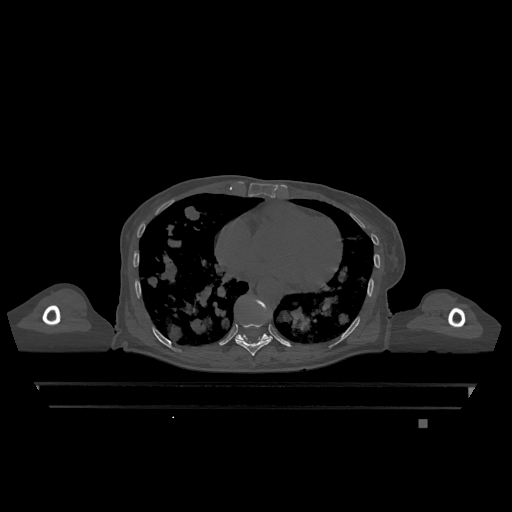
CT including the spine, one axial slice; slice 676 of 1317 in the series (ordered by position); bone window (W 1800 / L 400 HU); 512 × 512 image matrix, field of view 500 × 500 mm. Patient: female, 74 years. From the clinical record (not read from this slice): primary cancer: lung; vertebrae with lytic lesions (as recorded): T1, T4, T5, T6, L4, L5.
Annotated regions visible in this slice (semi-automatic segmentation, software-assisted and operator-edited):
- T10 vertebra: bounding box [x1, y1, x2, y2] px = [235, 299, 272, 340]
- T9 vertebra: [235, 307, 272, 356]